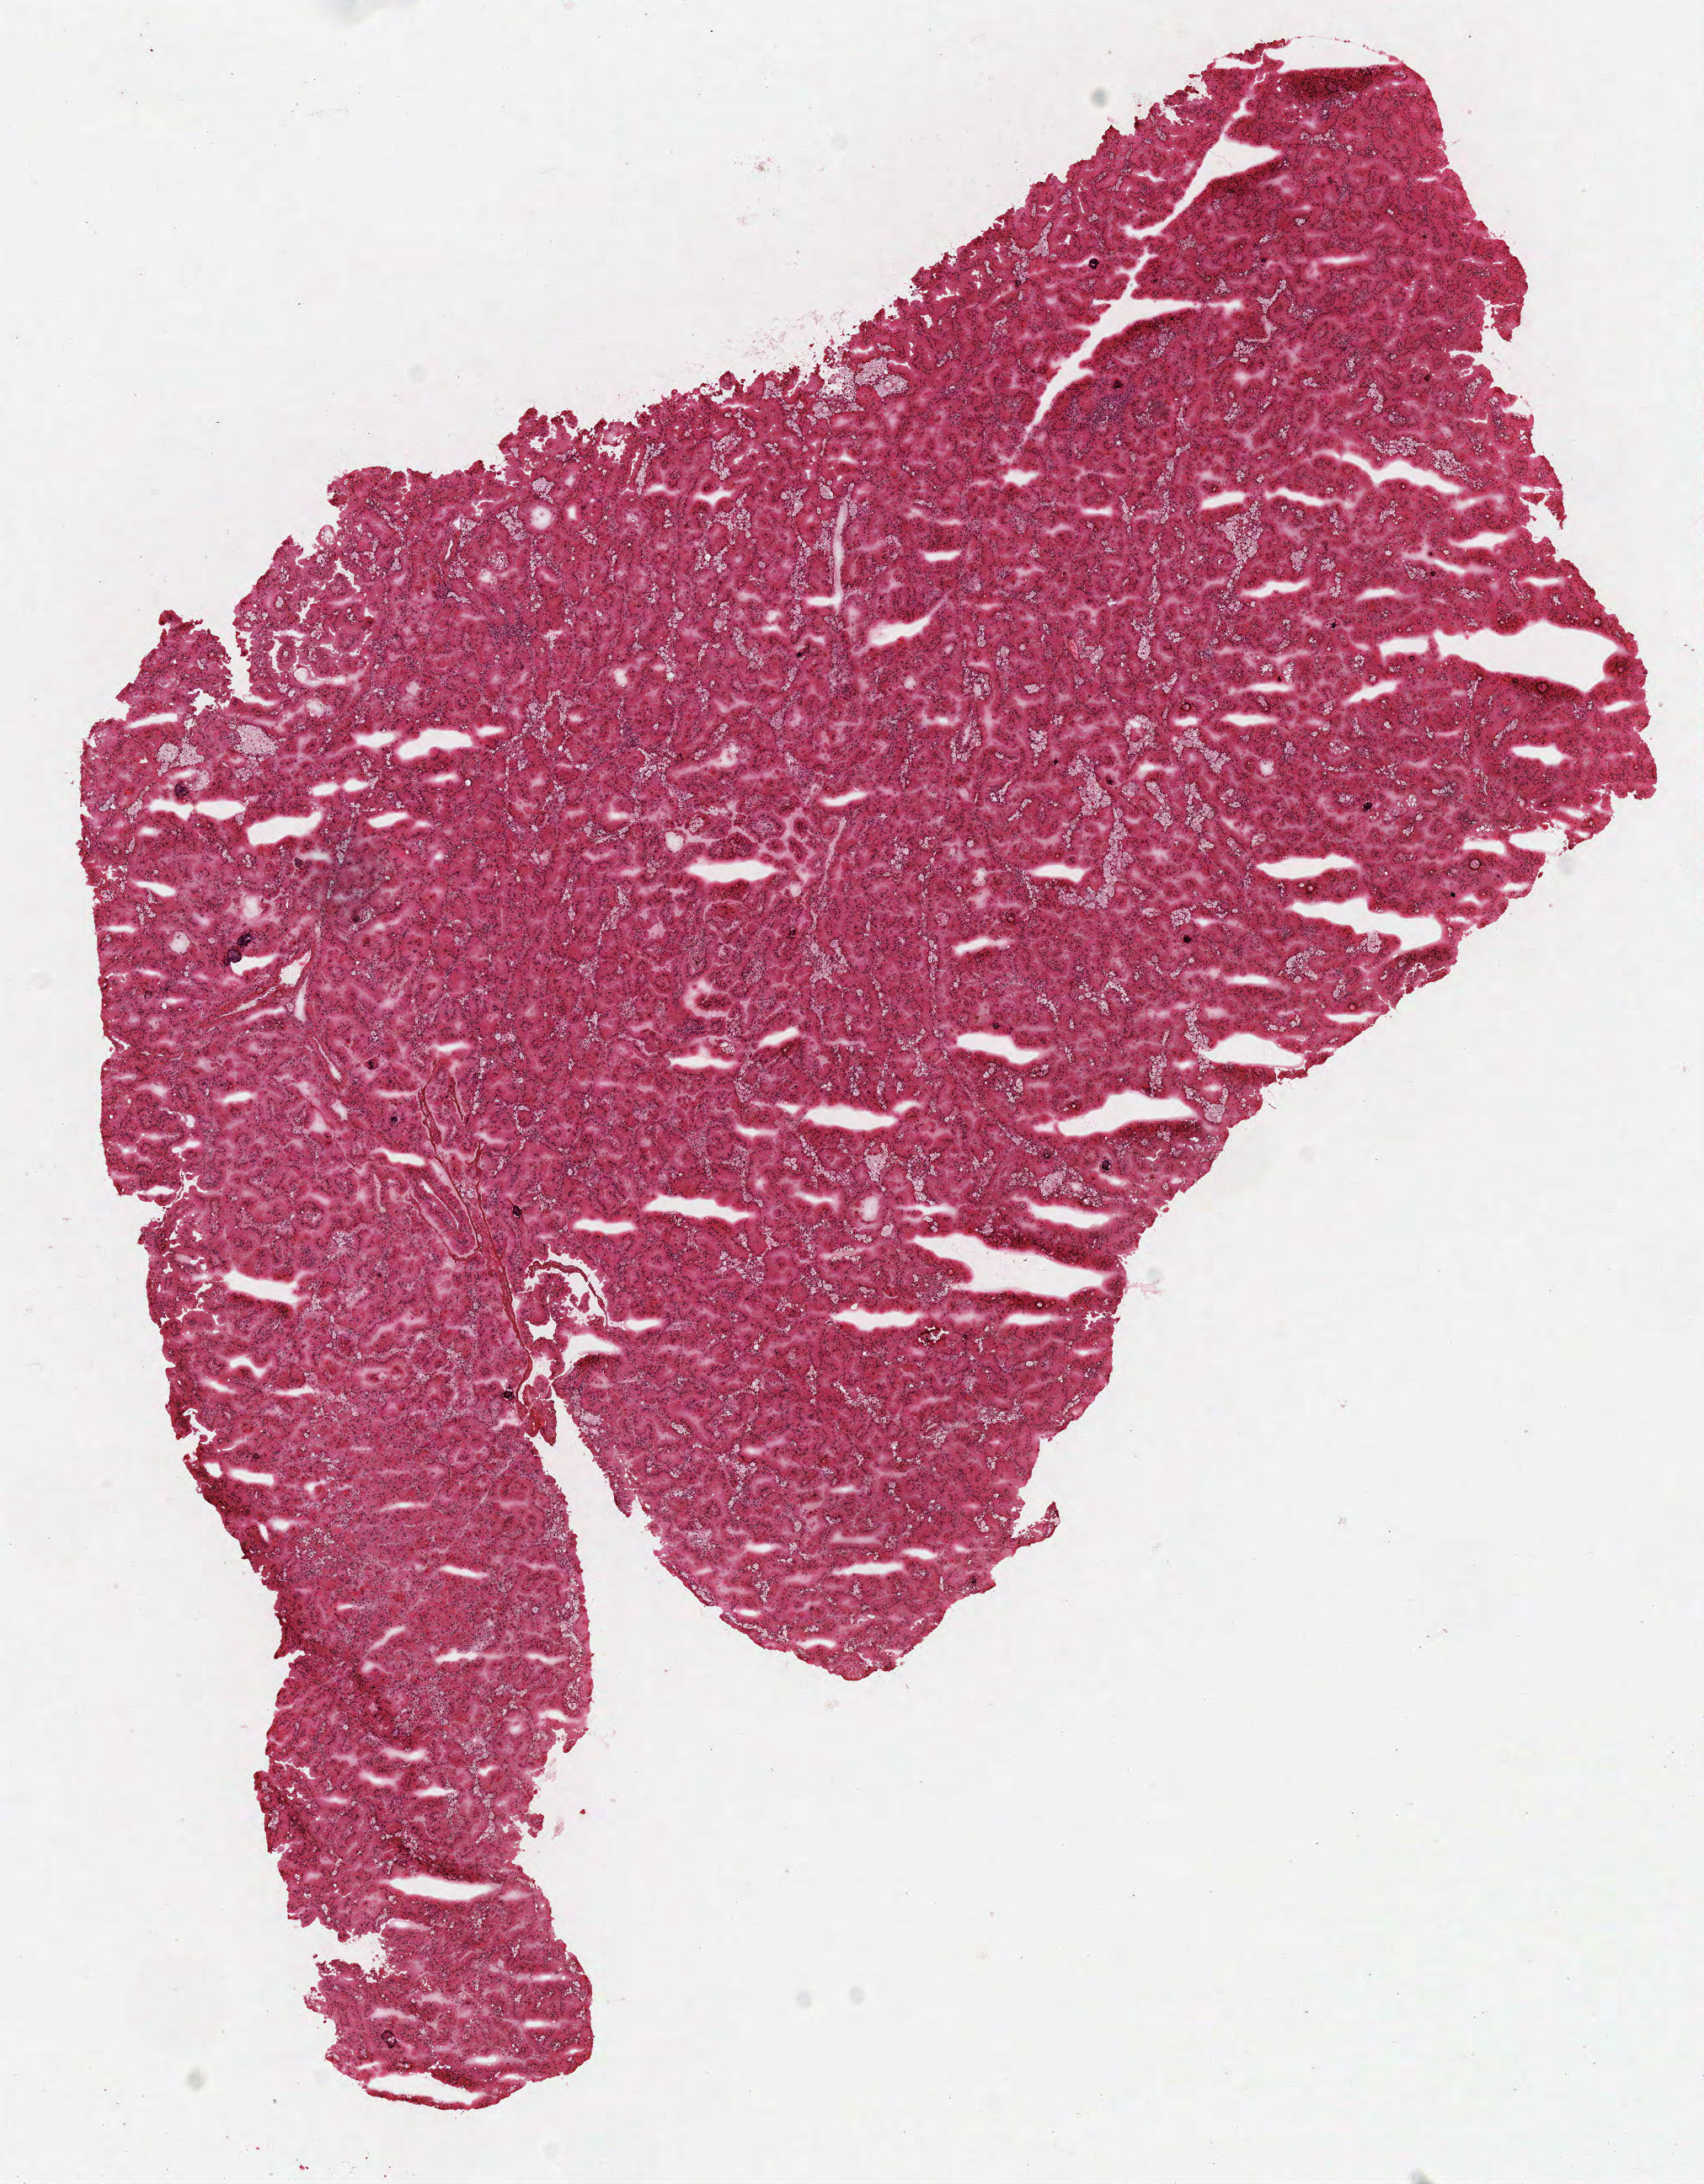
Digitized H&E tissue section (whole slide) — whole scanned area (about 8.0 x 10.2 mm, from a 40x scan) shown as a low-resolution overview; frozen section; sample: primary tumour, kidney. Female, age 59 years at initial diagnosis. Slide review estimates, as recorded: tumour cells 90%, tumour nuclei 85%, normal cells 0%, stromal cells 10%, necrosis 0%.
AJCC pathologic stage: I. Pathologic diagnosis: Papillary adenocarcinoma, NOS. TNM: T1a NX M0. Laterality: right.